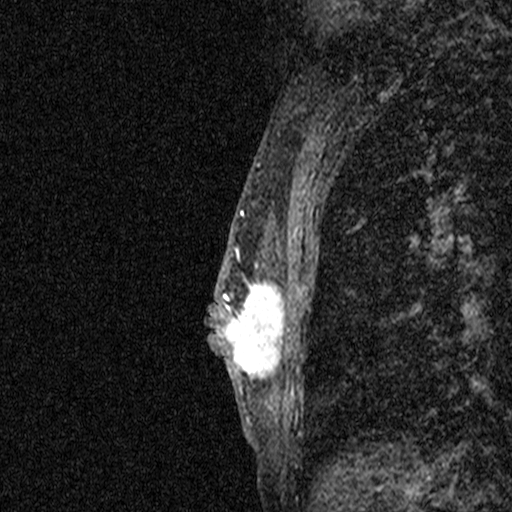
Breast MRI (dynamic contrast-enhanced), one sagittal slice. Dynamic contrast-enhanced study with each time point stored as its own series, time point 2 of 3 at this slice position (early post-contrast, ordered by acquisition time). 1.5 T. TE 4.5 ms, TR 11 ms. 2.05 mm slice thickness. 512 × 512 image matrix, field of view 200 × 200 mm. Female patient, age 44 years. Case-level facts recorded for this patient, not image findings: setting: breast cancer imaged before/during neoadjuvant chemotherapy; receptor status: HR-positive, HER2-negative.
Outlined on this slice (semi-automatic segmentation, software-assisted and operator-edited):
- analysis volume of interest (the breast-tissue region the enhancement analysis was run in; not a lesion): bounding box (x1, y1, x2, y2) in pixels: (204, 254, 282, 401)
- tumour enhancement mask (voxels above the 90 % enhancement threshold inside the analysis volume of interest): (206, 254, 282, 395)